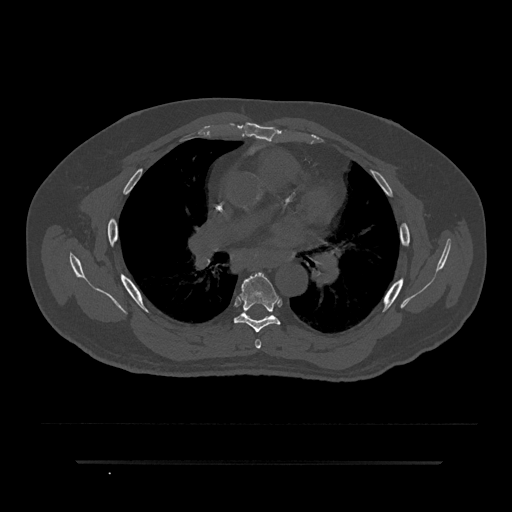
CT including the spine, one axial slice. Position 530 of 797 along the scan axis. Bone window (W 1800 / L 400 HU). 0.5 mm slice thickness. 512 × 512 image matrix. Patient: male, 59 years. Case-level facts recorded for this patient, not image findings: primary cancer: bile ducts; vertebrae with lytic lesions (as recorded): T10.
Structures marked on this image (semi-automatically segmented with operator editing):
- T5 vertebra: bounding box (x1, y1, x2, y2) in pixels: (255, 339, 262, 349)
- T6 vertebra: (233, 273, 281, 333)